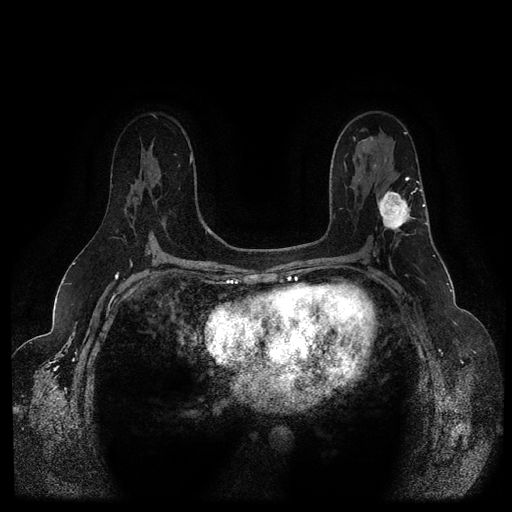
Breast MRI (dynamic contrast-enhanced, multi-phase), one axial slice. Position 62 of 116 along the scan axis. Dynamic contrast-enhanced series, time point 2 of 5 at this slice position (early post-contrast). 1.5 T. TE 2.6 ms, TR 5.3 ms. 2 mm slice thickness. 512 × 512 image matrix, field of view 350 × 350 mm. Female patient, age 54 years.
Structures marked on this image (semi-automatically segmented with operator editing):
- breast lesion (labelled 'tumour' in the annotation; benign lesions carry a separate 'benign' label): bounding box (x1, y1, x2, y2) in pixels: (376, 187, 414, 236)